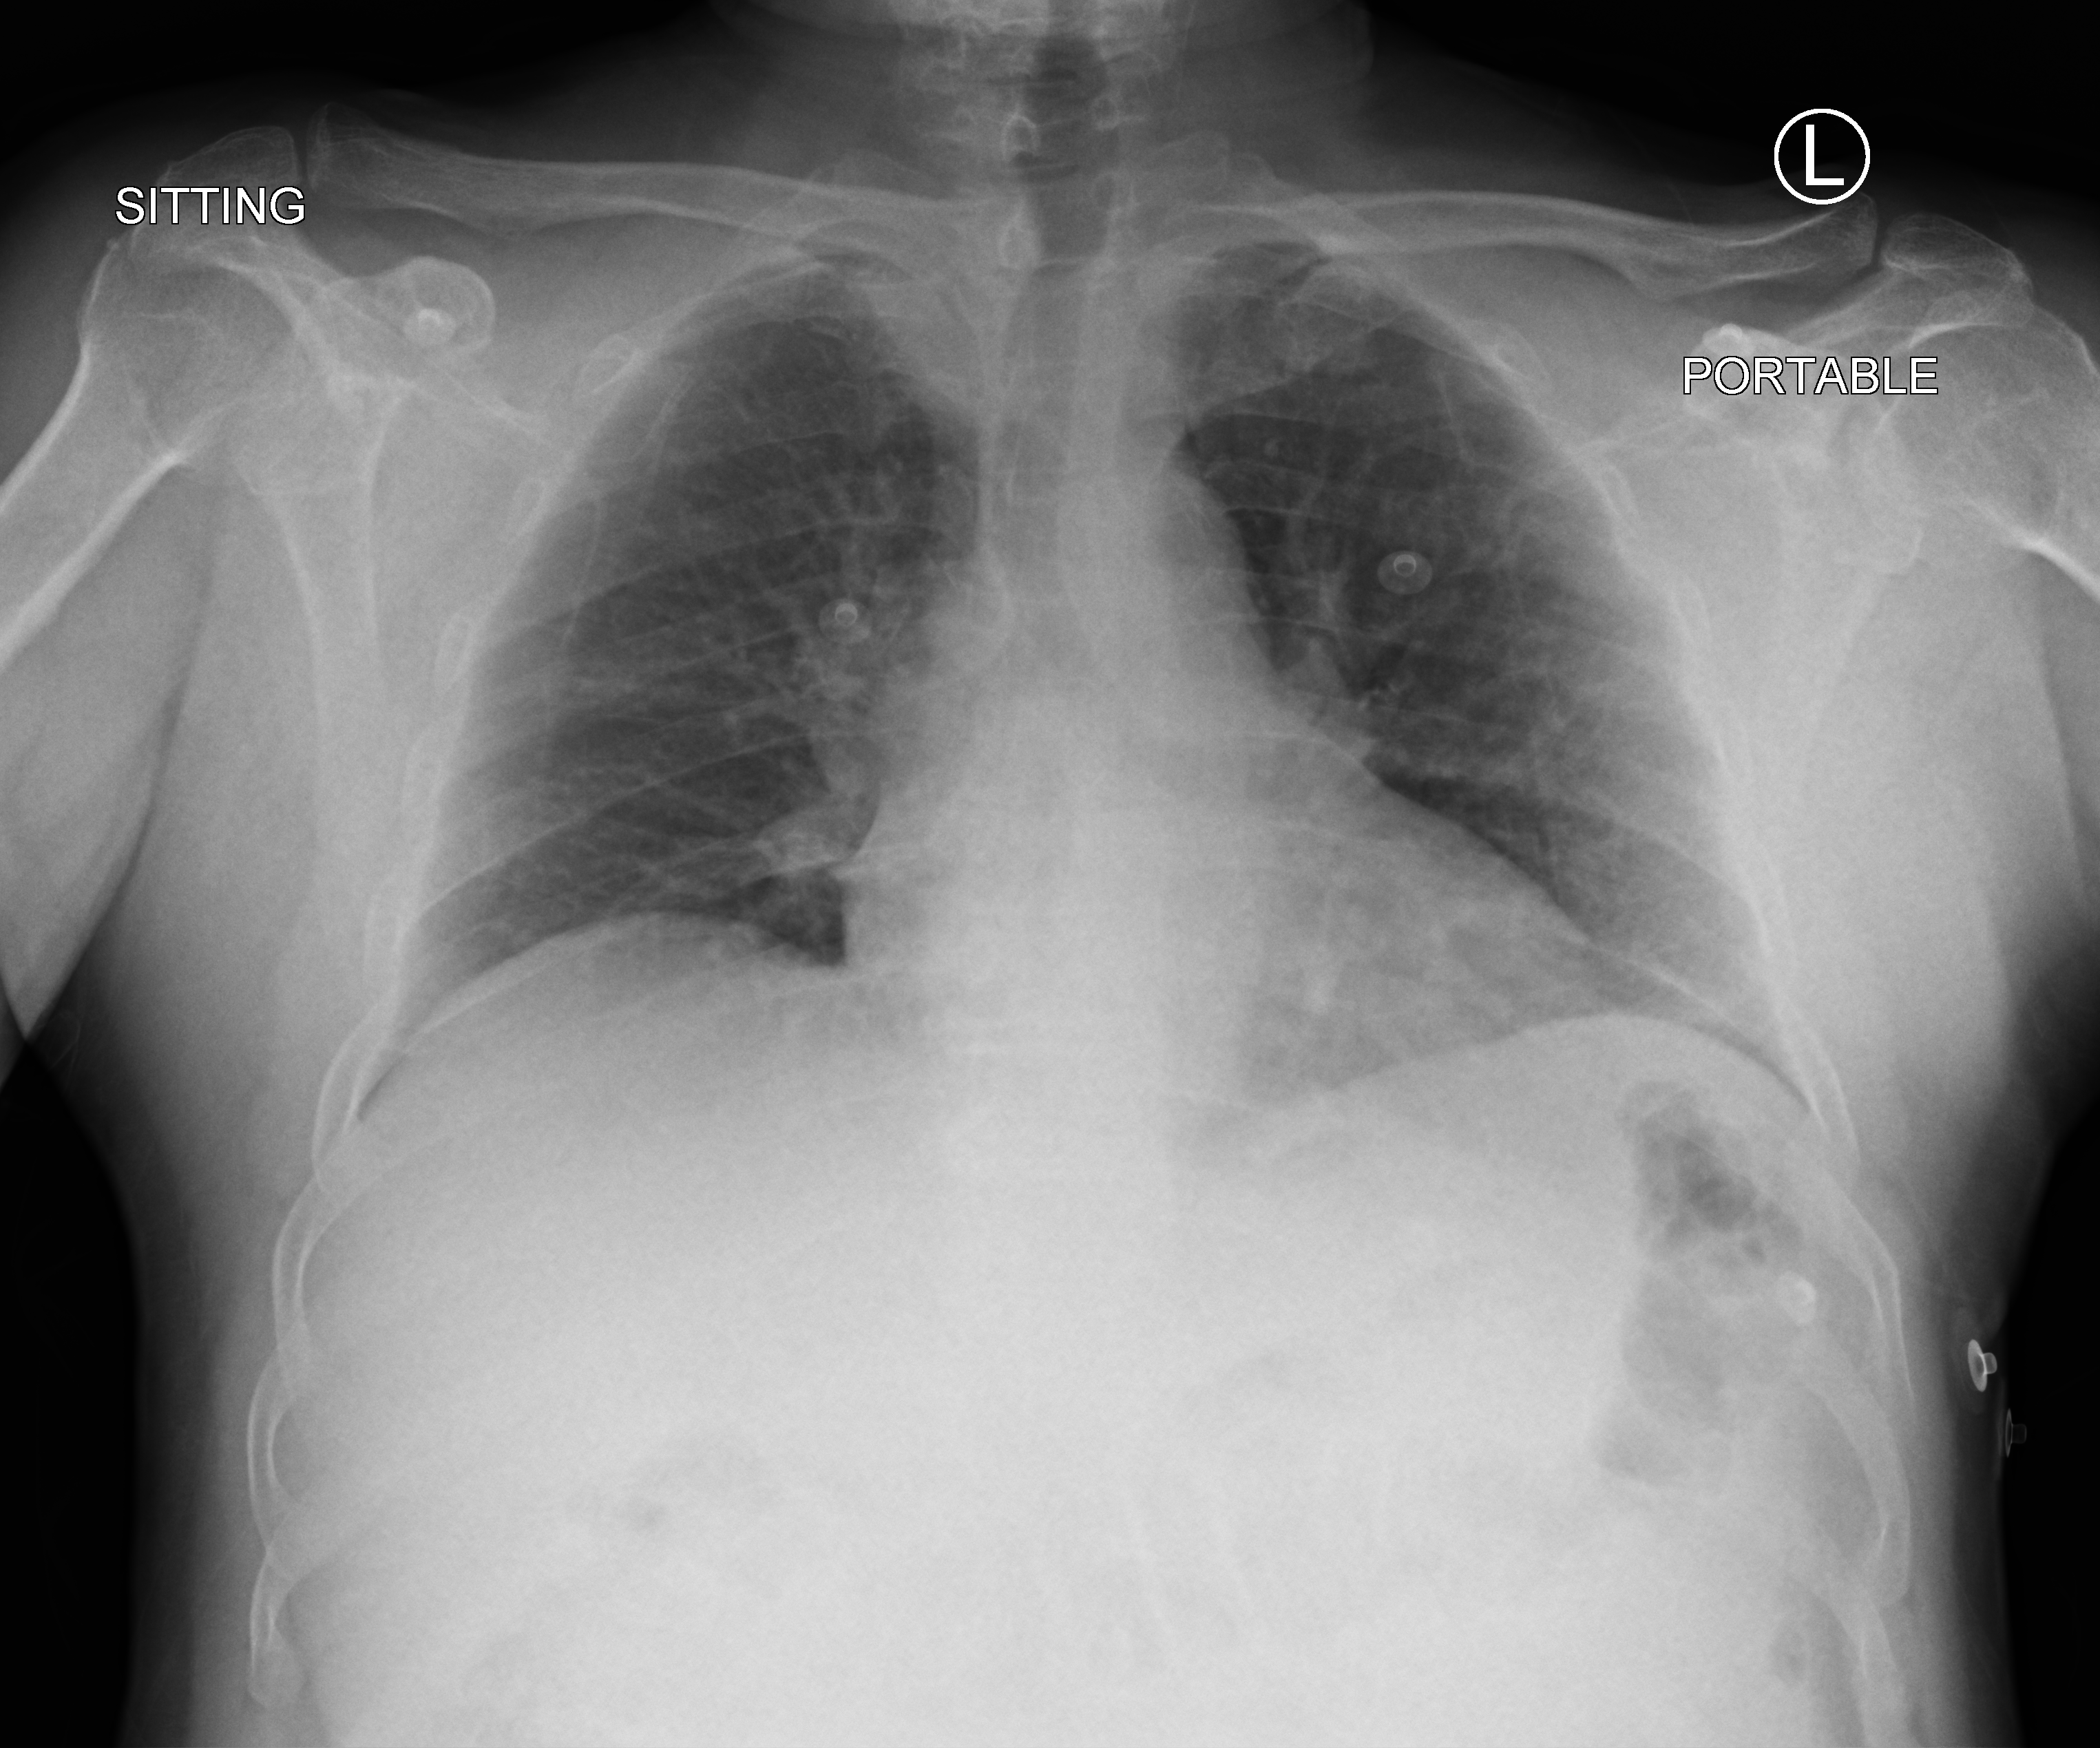
Portable chest radiograph, anteroposterior (AP) projection. Male patient hospitalised with COVID-19, age 60–74 years.
From the hospital-stay record, not from the radiograph (when in the stay this image was taken is not recorded):
- admitted to intensive care during this hospital stay: no
- mechanically ventilated during this hospital stay: no